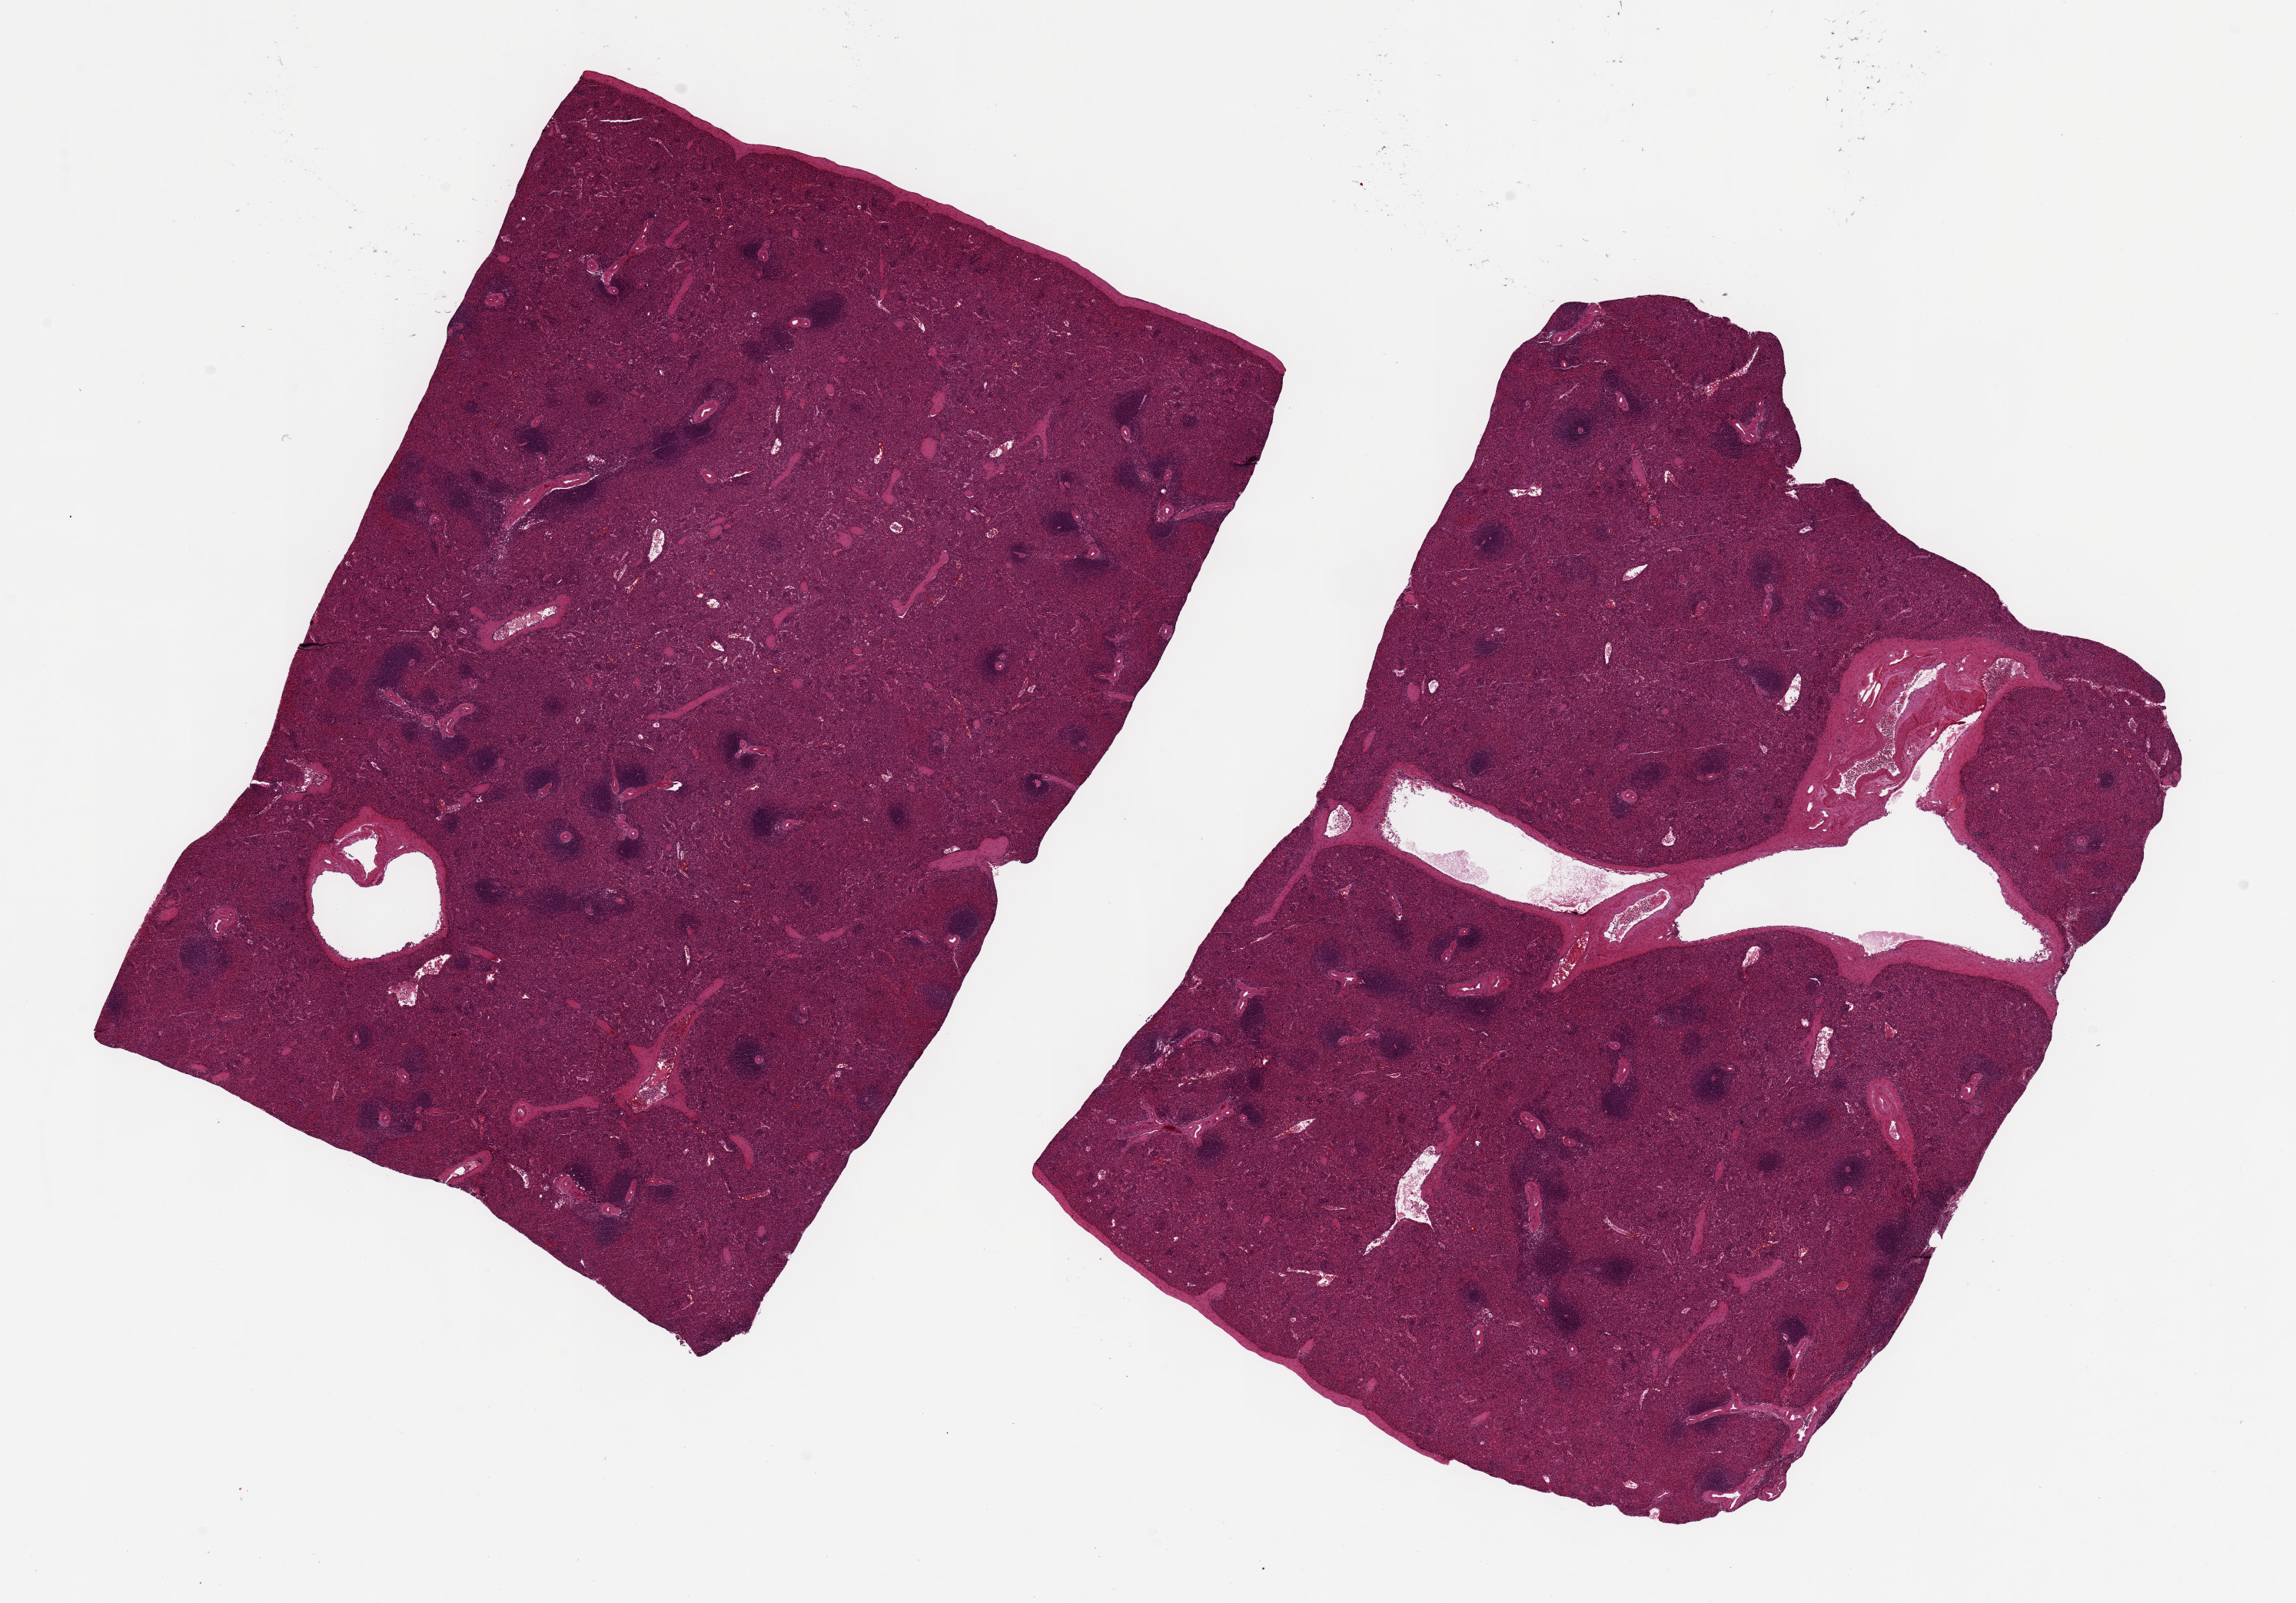
Whole-slide image, hematoxylin and eosin (H&E) stain — low-resolution overview of the scanned area, about 23.6 x 16.5 mm (slide scanned at 20x); PAXgene-fixed, paraffin-embedded tissue; sampled site (target tissue): spleen; donor tissue sample.
Pathologist's review note for this sample: 2 pieces ~11x8 mm; low lymphoid content.